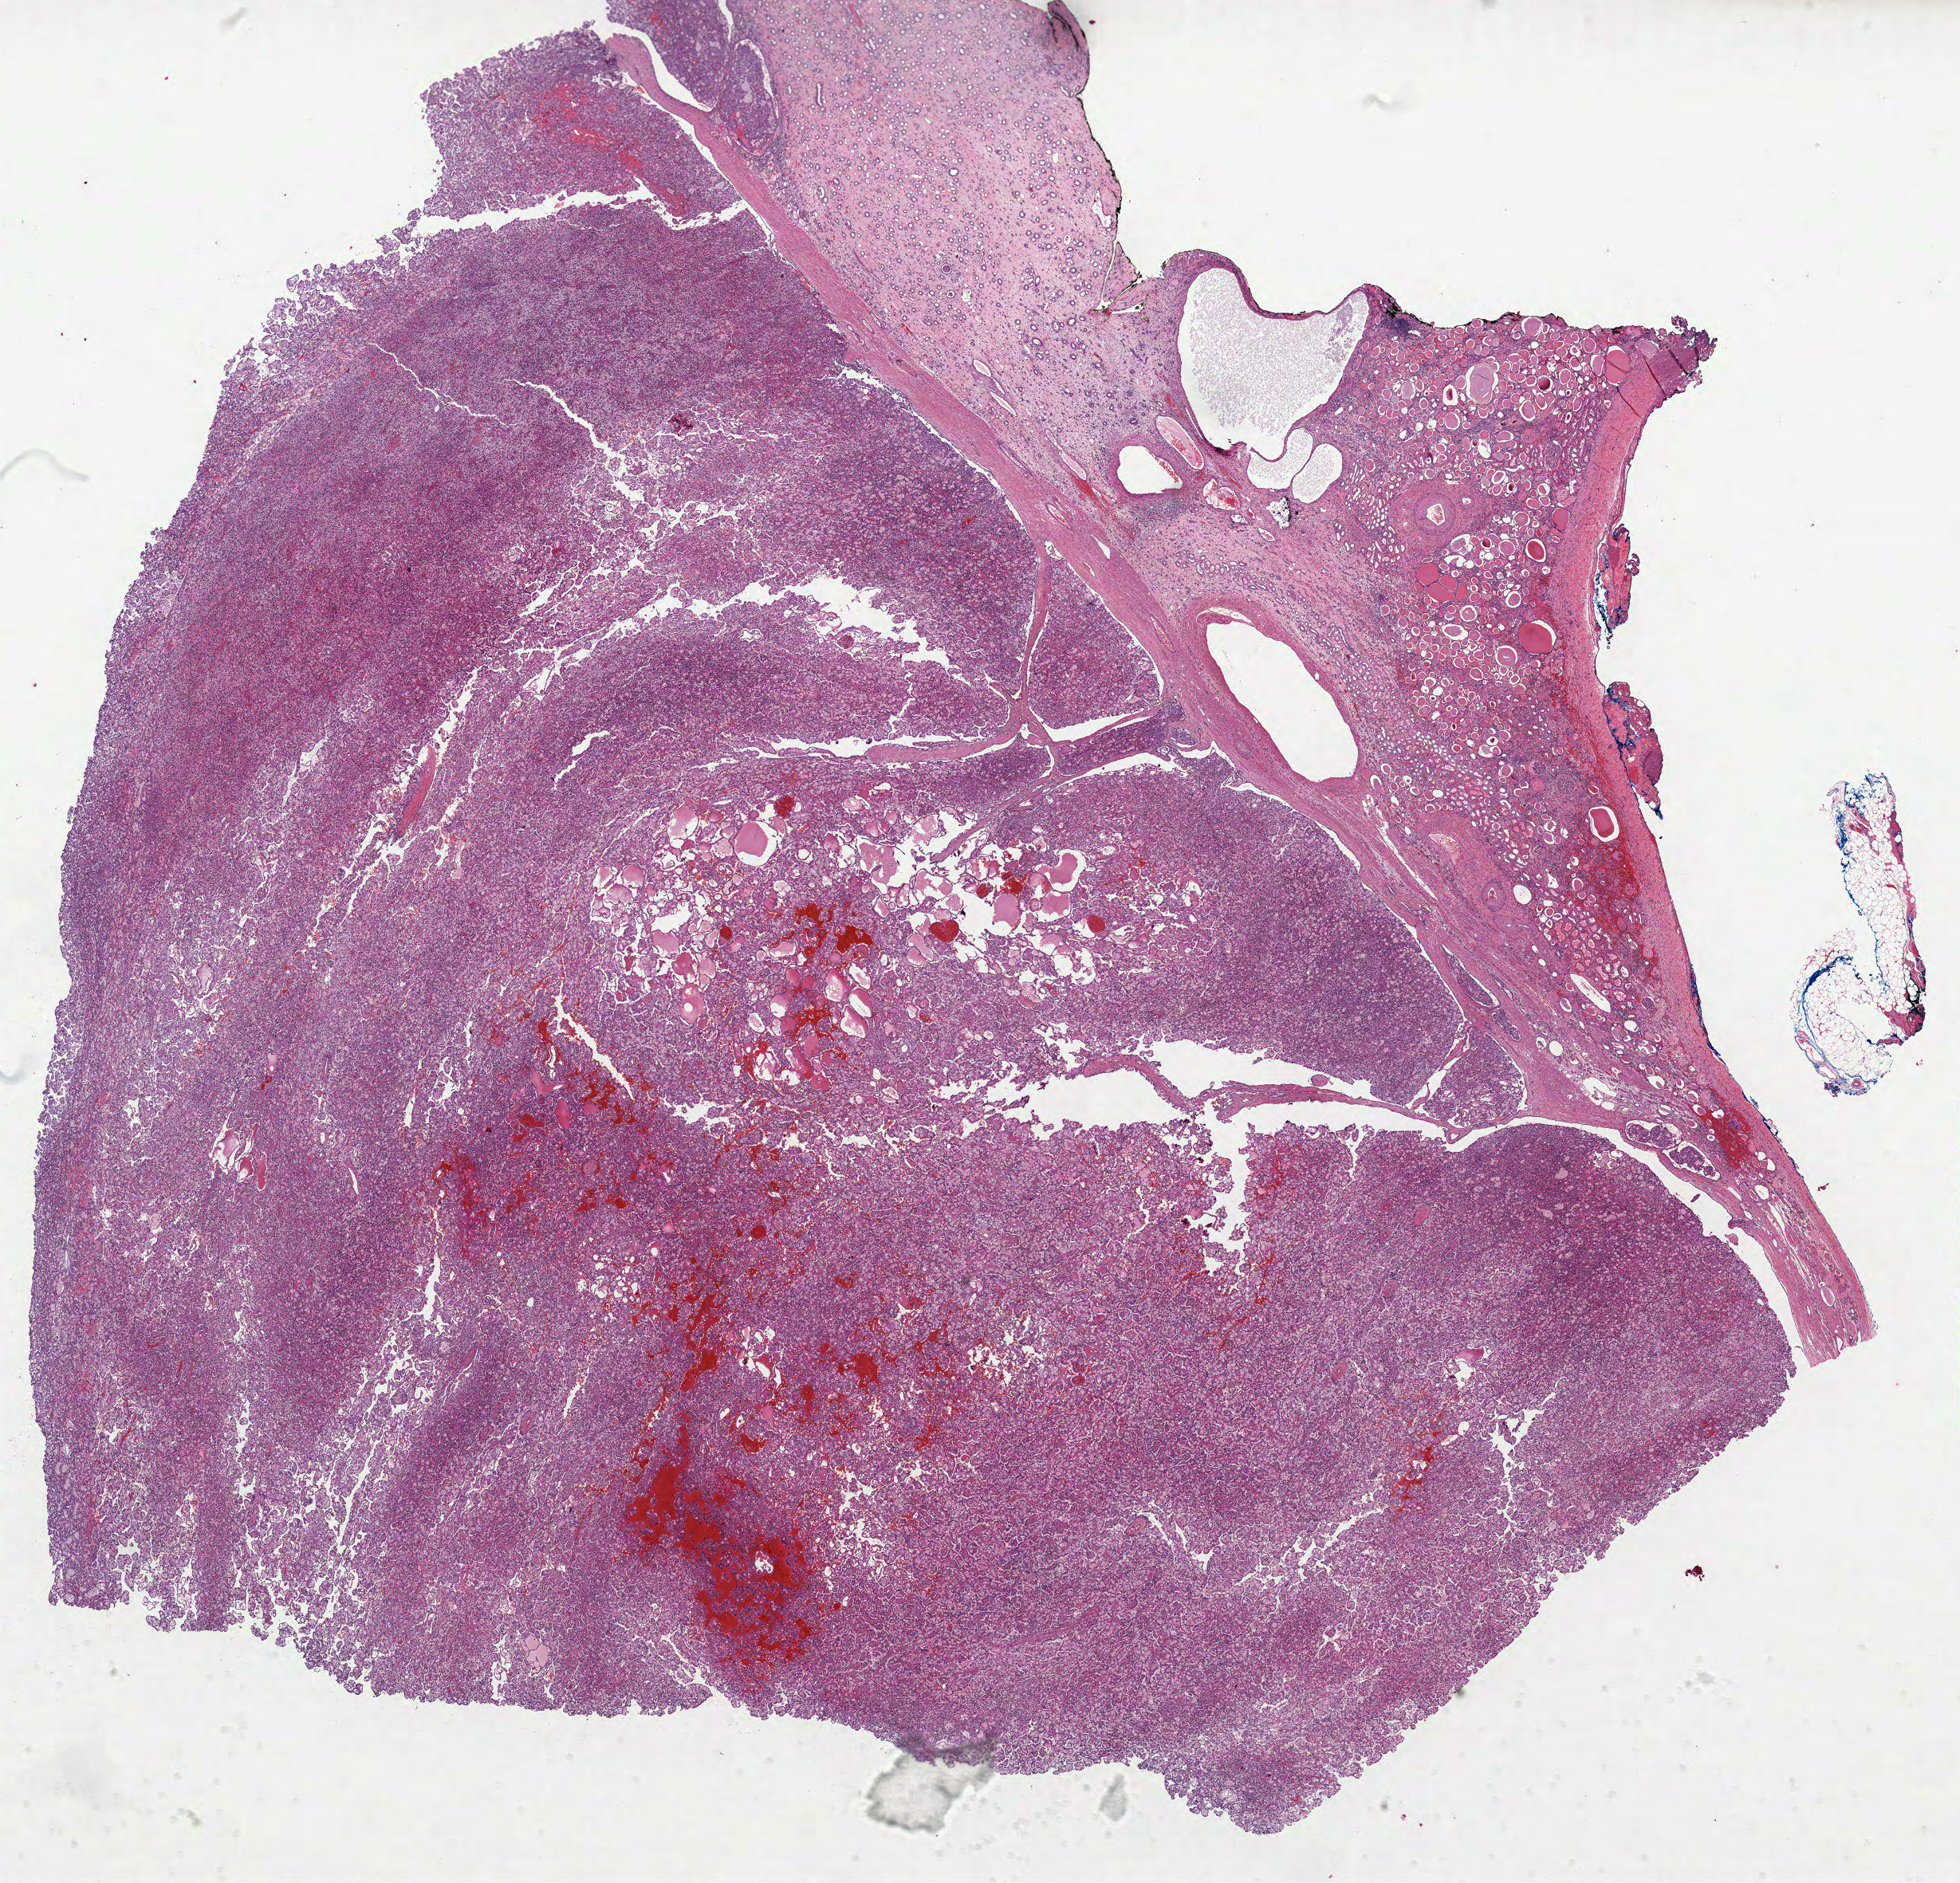
H&E-stained whole-slide image, shown as a low-resolution overview of the whole scanned area (about 19.8 x 19.0 mm, slide scanned at 40x), formalin-fixed paraffin-embedded (FFPE) diagnostic section, kidney, primary tumour sample. Female, age 60 years at initial diagnosis.
Histologic diagnosis: Papillary adenocarcinoma, NOS.